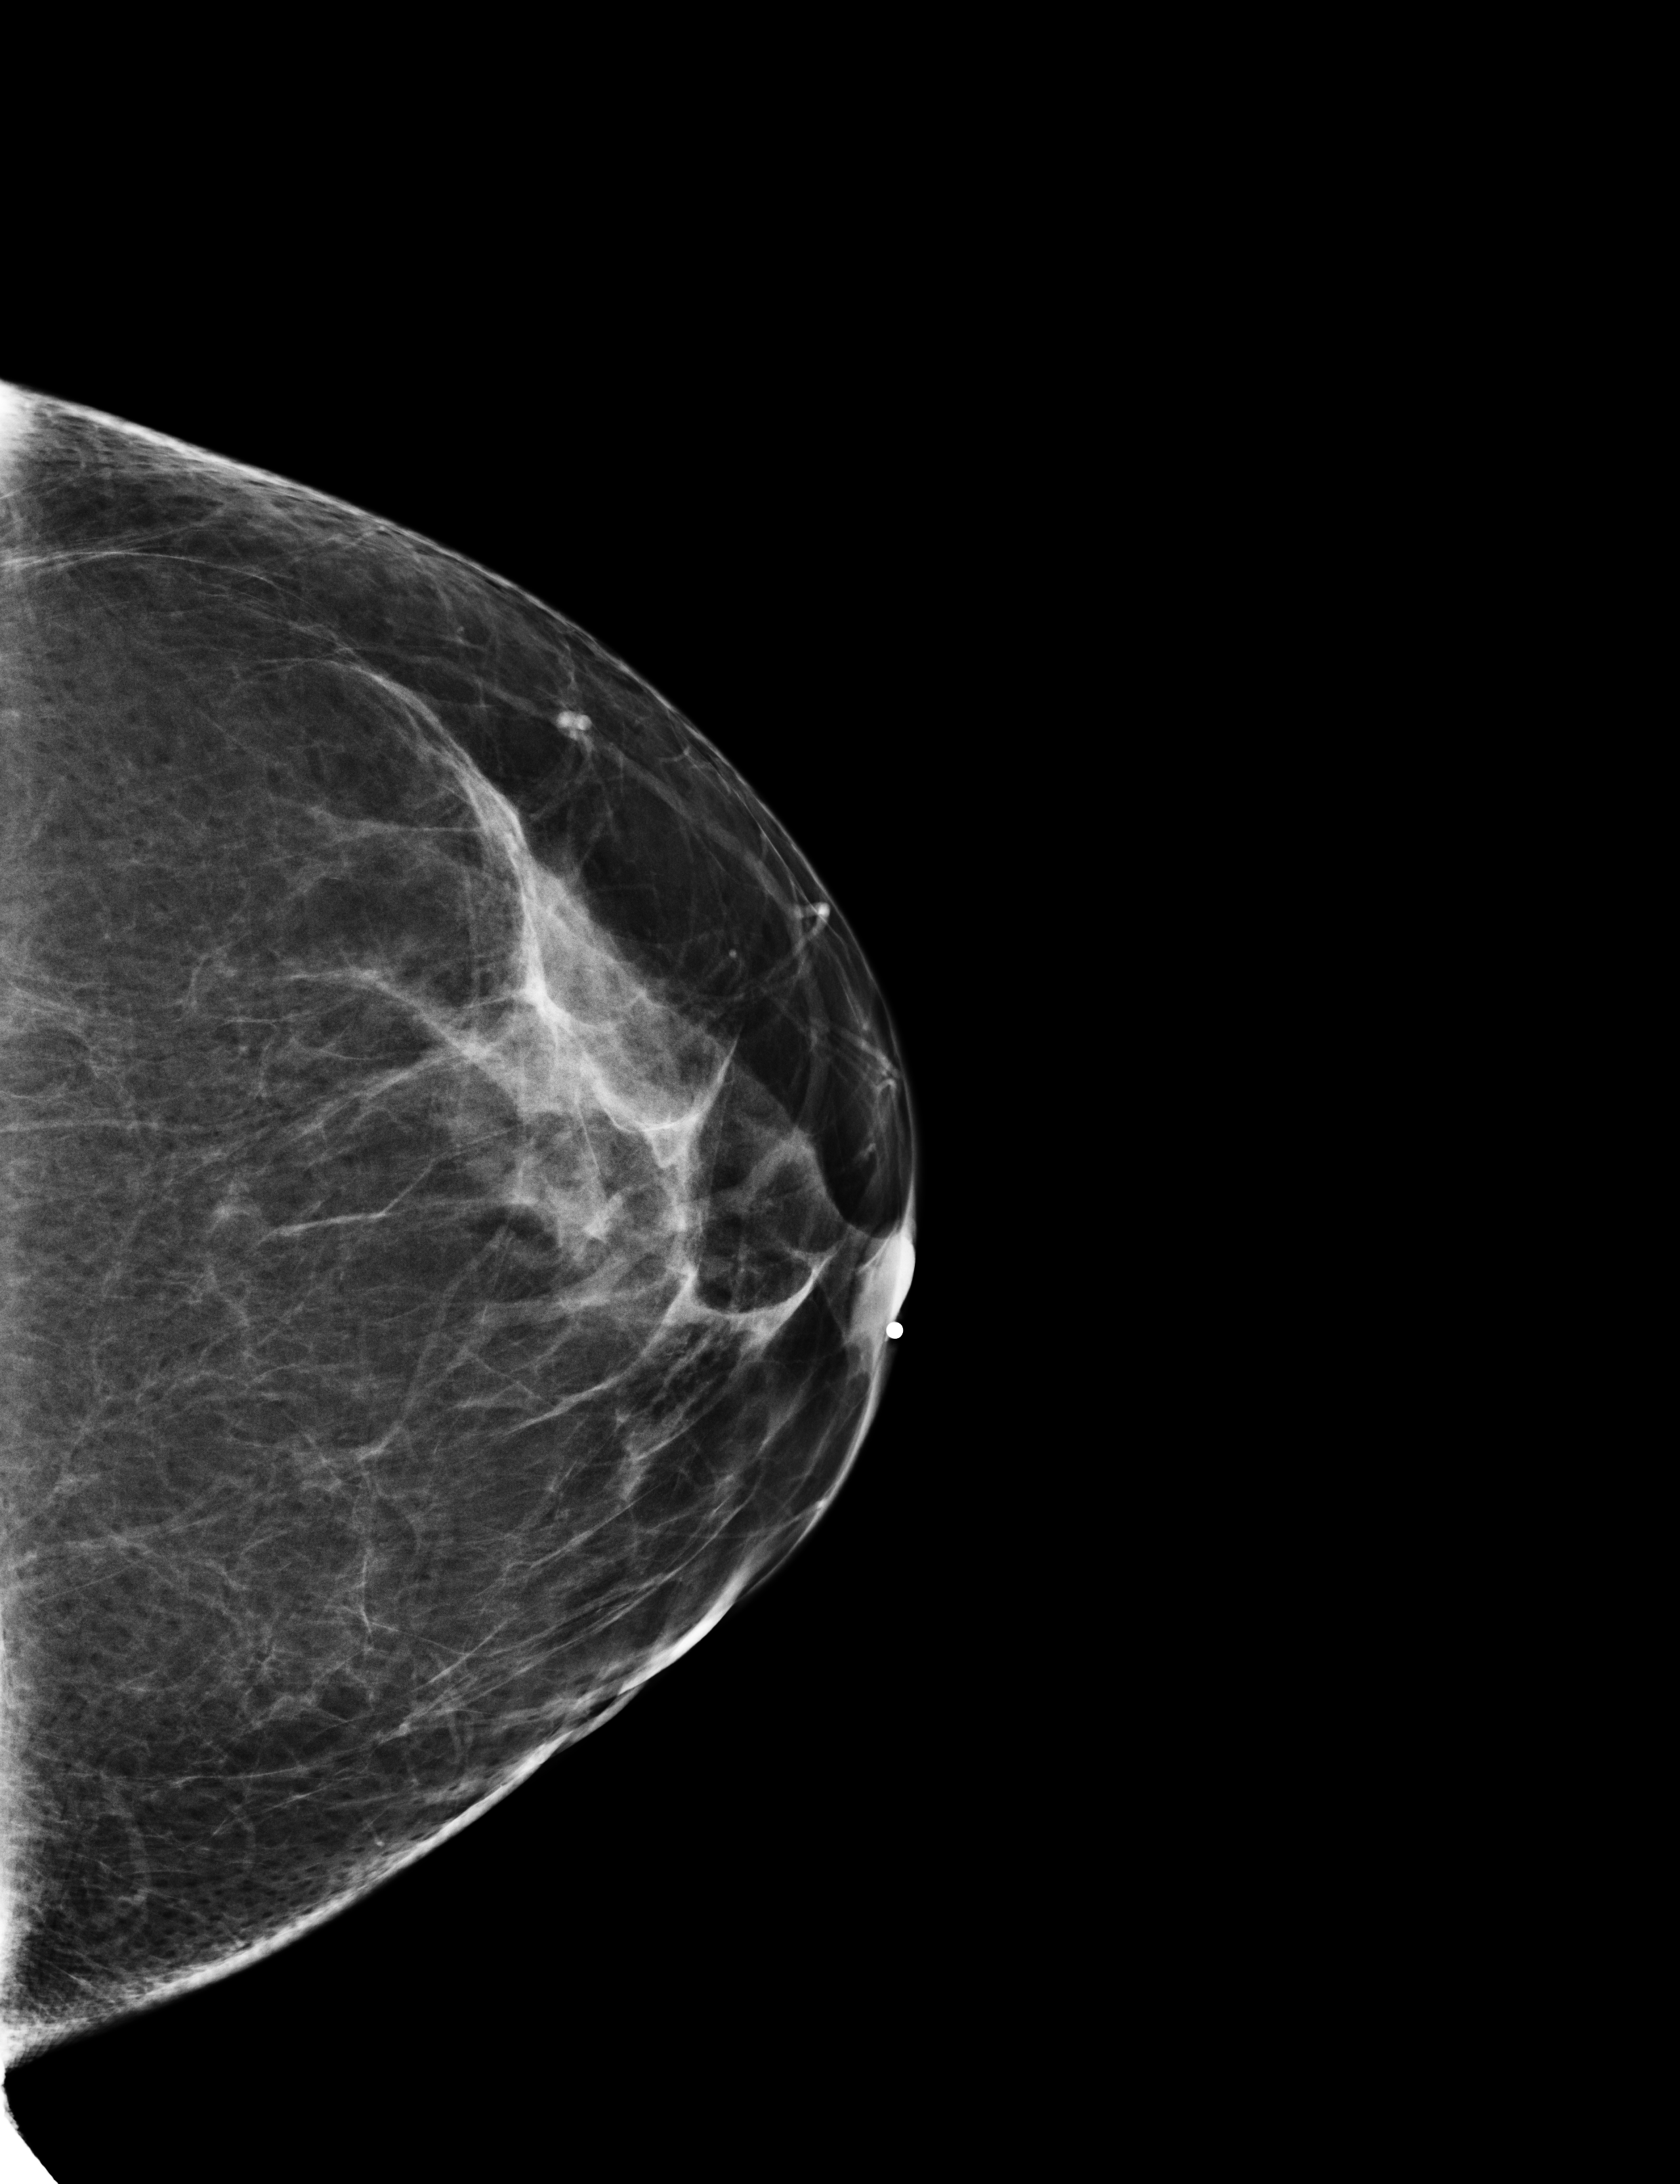
Annual screening mammography examination, compressed breast thickness 71 mm. Patient: female, 50 years.
Image type: full-field digital mammogram. Breast: left. Projection: craniocaudal (CC) view.